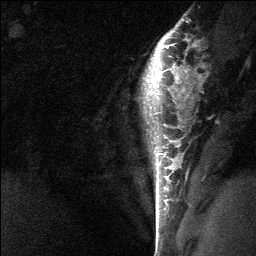
Breast MRI (dynamic contrast-enhanced), one sagittal slice; slice 53 of 64 in the series (ordered by position); dynamic contrast-enhanced study with each time point stored as its own series, time point 2 of 3 at this slice position (early post-contrast, ordered by acquisition time); 1.5 T; TE 4.8 ms, TR 27 ms; 256 × 256 image matrix, field of view 180 × 180 mm. Female patient, age 26 years. From the clinical record (not read from this slice): setting: breast cancer imaged before/during neoadjuvant chemotherapy; receptor status: HR-positive, HER2-negative.
Structures marked on this image (semi-automatic segmentation, software-assisted and operator-edited):
- analysis volume of interest (the breast-tissue region the enhancement analysis was run in; not a lesion): bounding box <142,43,183,138> (left, top, right, bottom; pixels)
- tumour enhancement mask (voxels above the 90 % enhancement threshold inside the analysis volume of interest): <166,46,168,48>